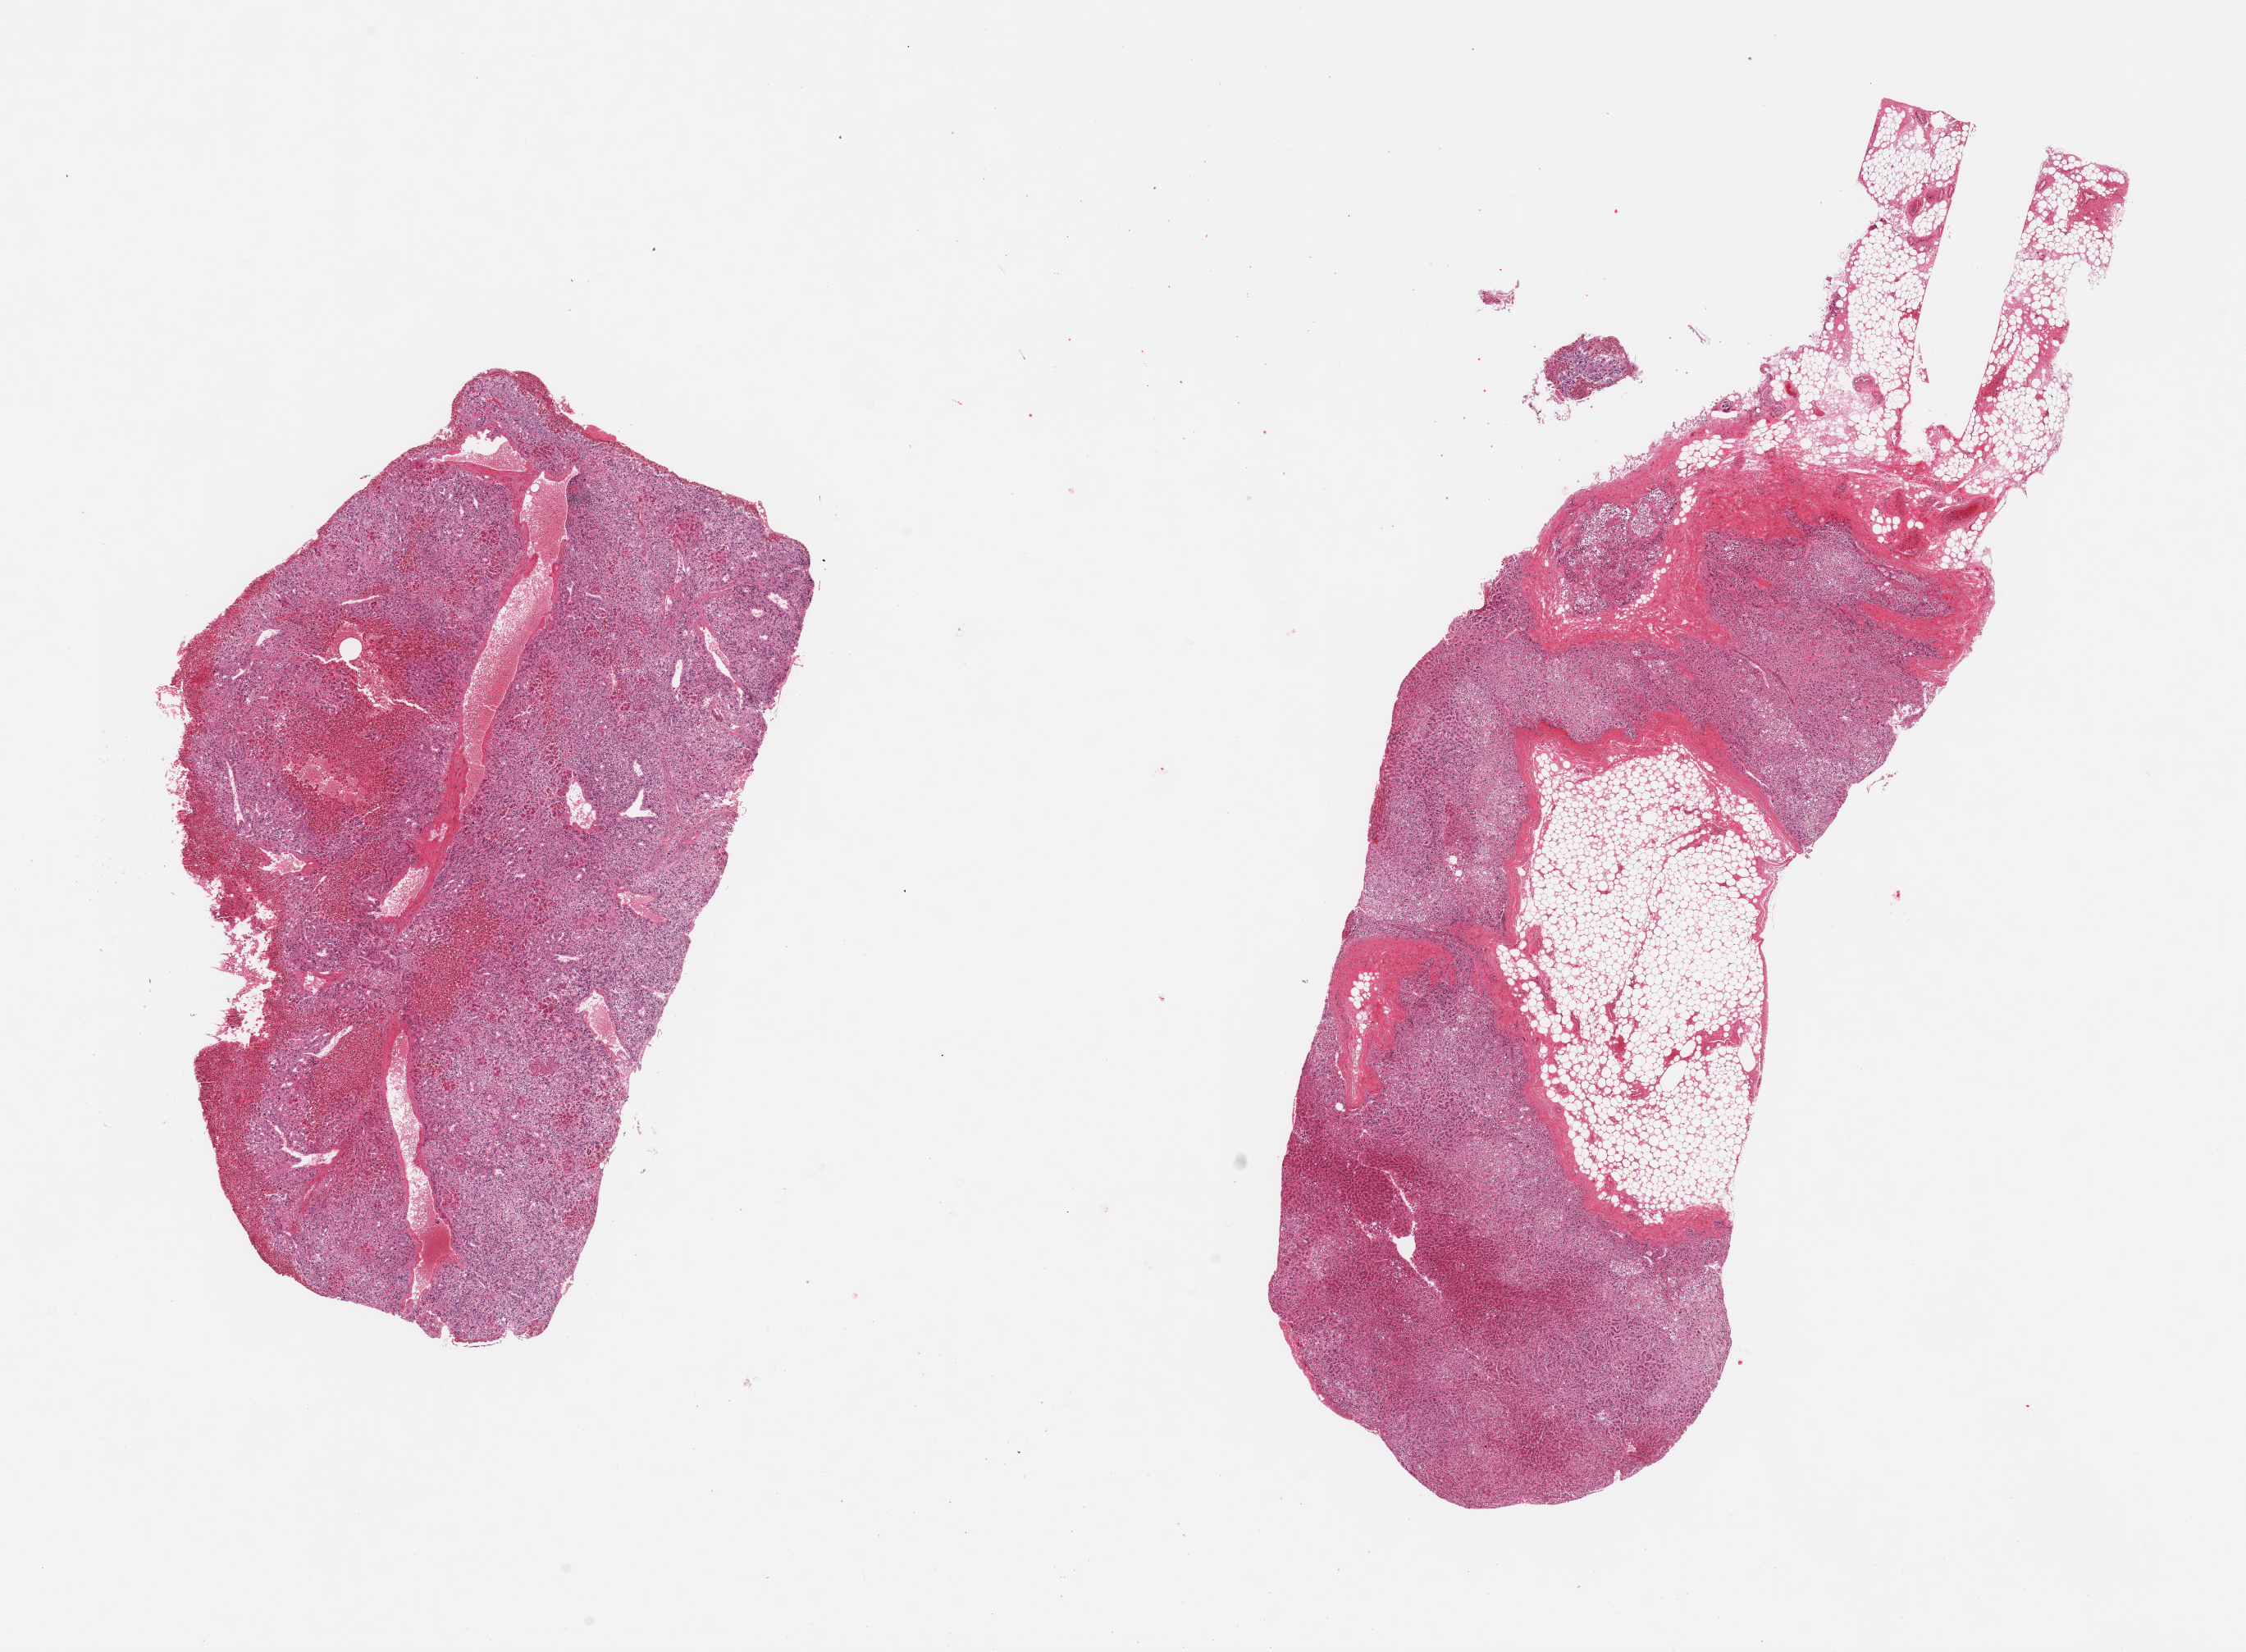
Whole-slide image, haematoxylin and eosin stain, low-resolution overview of the scanned area, about 21.7 x 15.9 mm (from a 20x scan). PAXgene-fixed paraffin-embedded (PFPE) section. Section of adrenal gland (target tissue). Tissue donor sample.
Review note (as recorded): 2 pieces, cortex, ~15-20% adherent/interstitial fat.